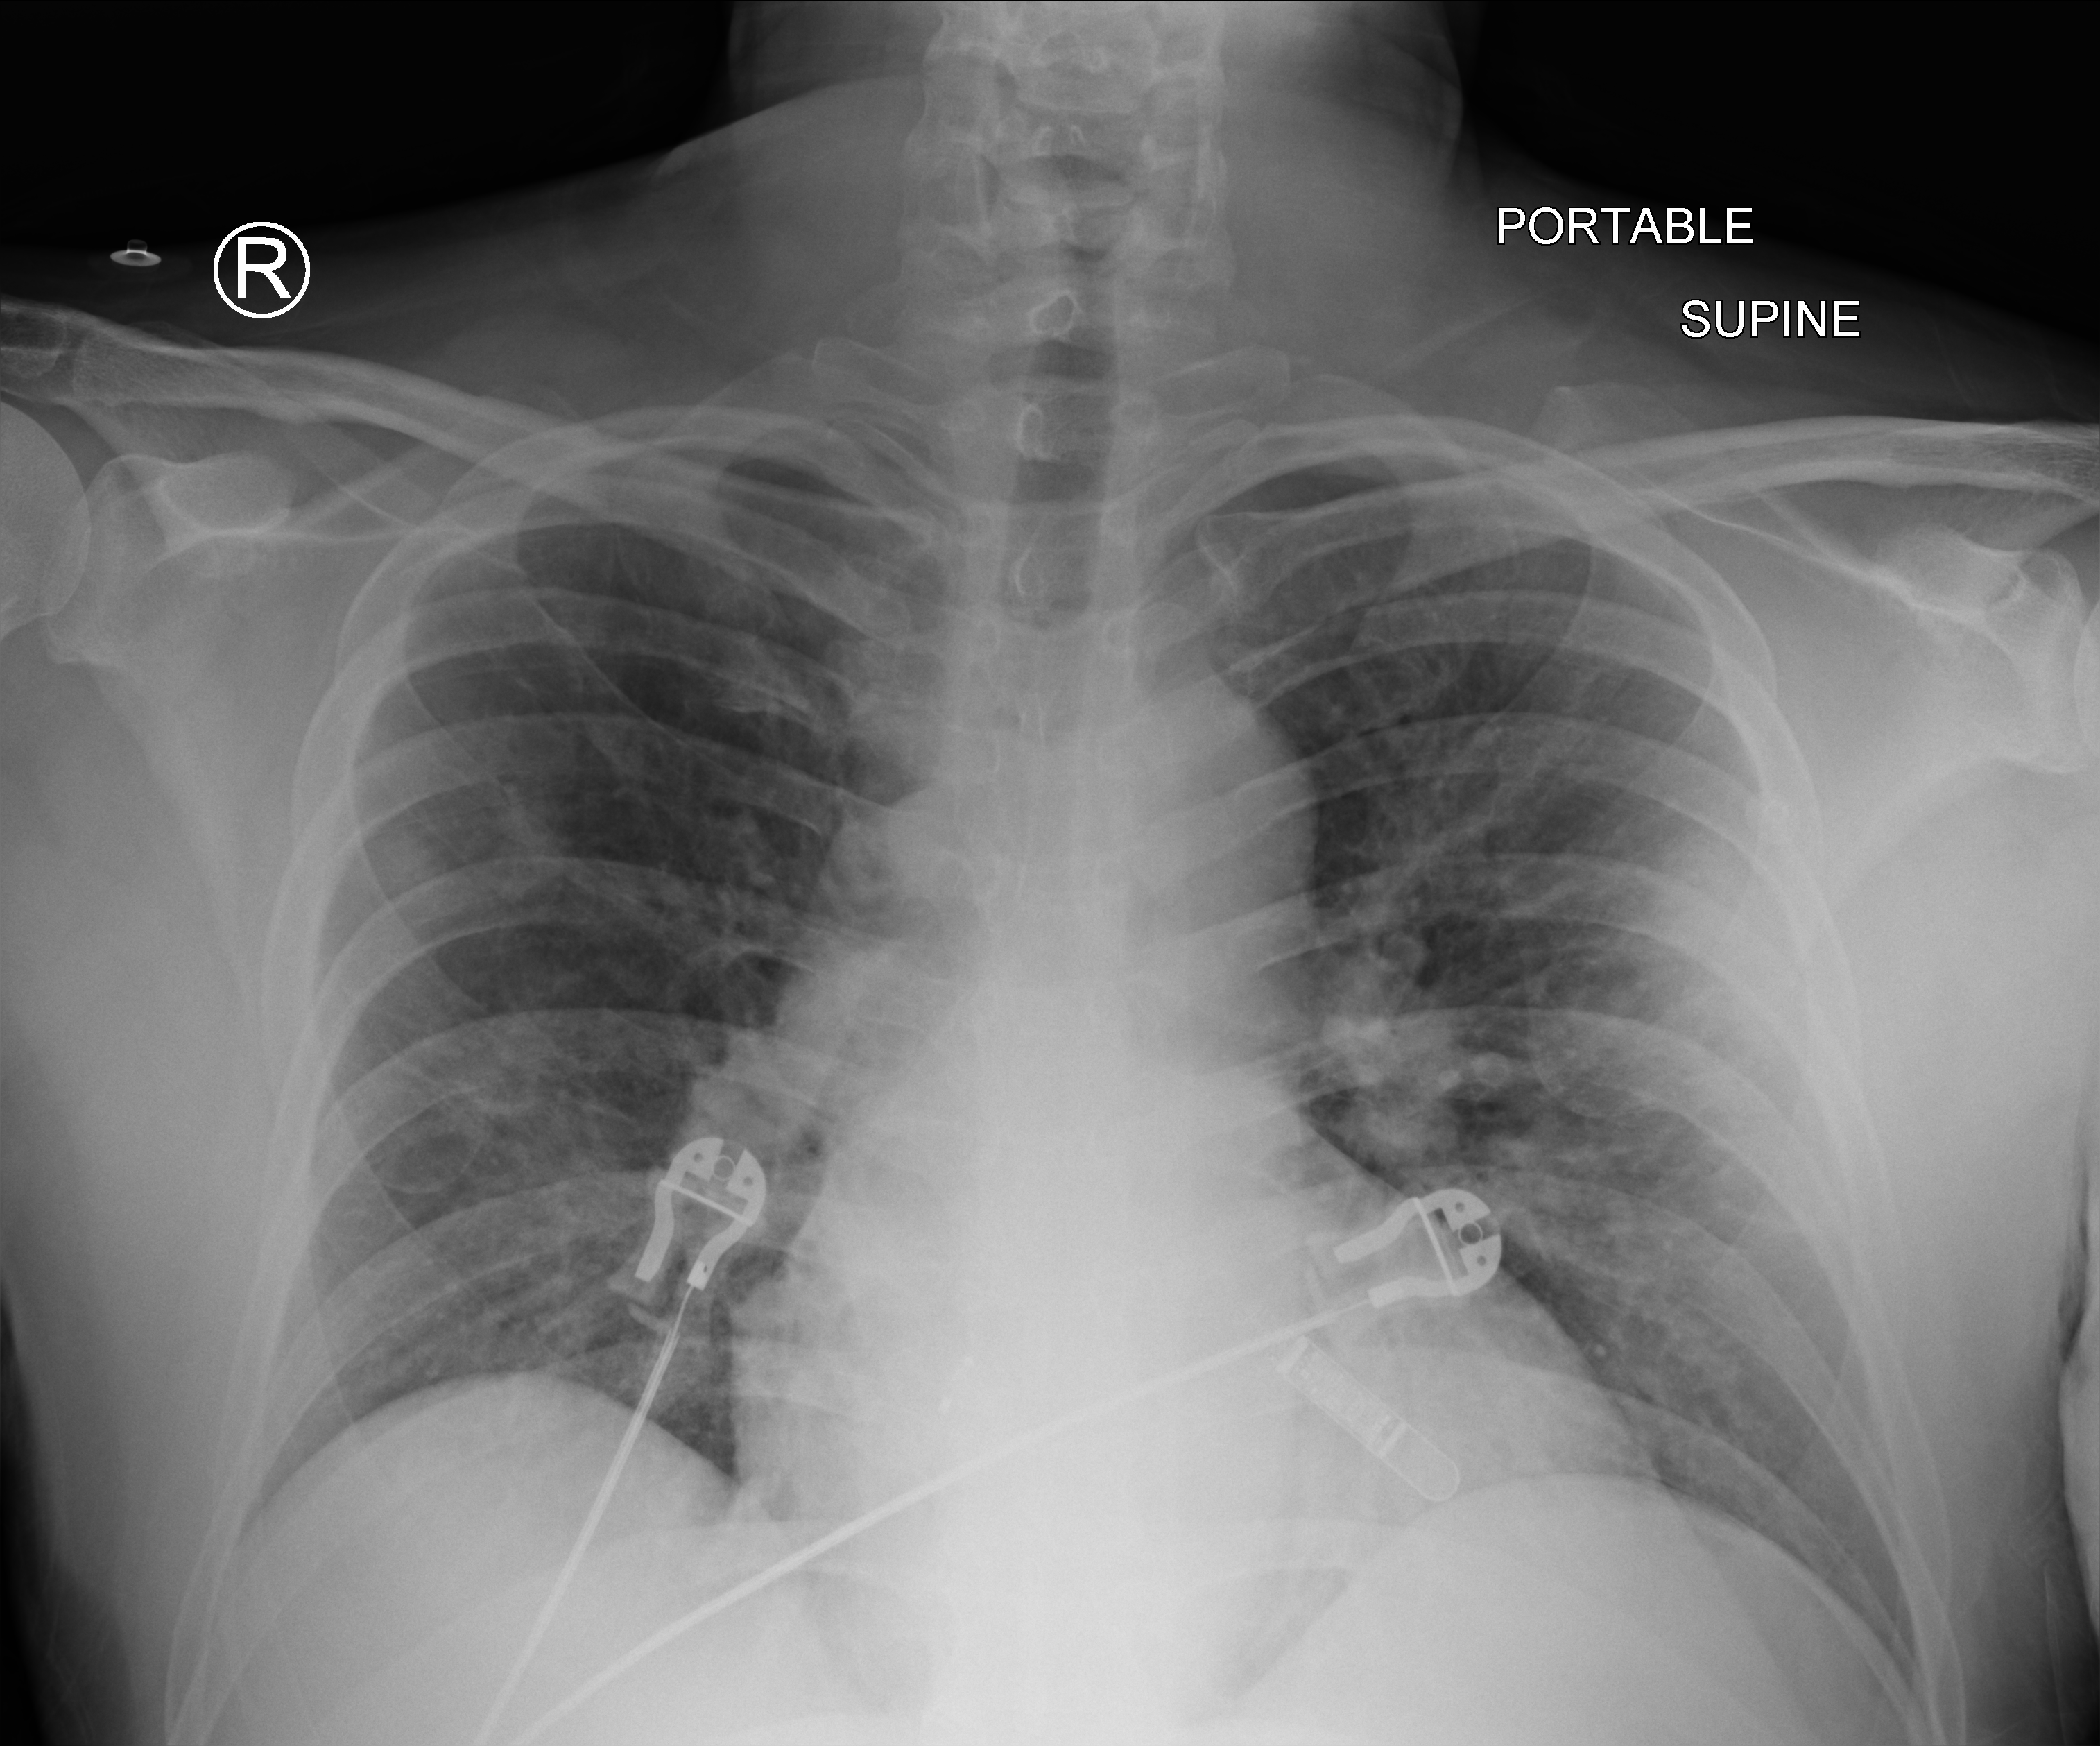
Bedside chest radiograph (computed radiography). Patient hospitalised with COVID-19; male, aged 18–59 years.
Hospital-stay facts (about this admission, not read from this image; timing relative to this image not recorded):
- length of hospital stay: 5 days